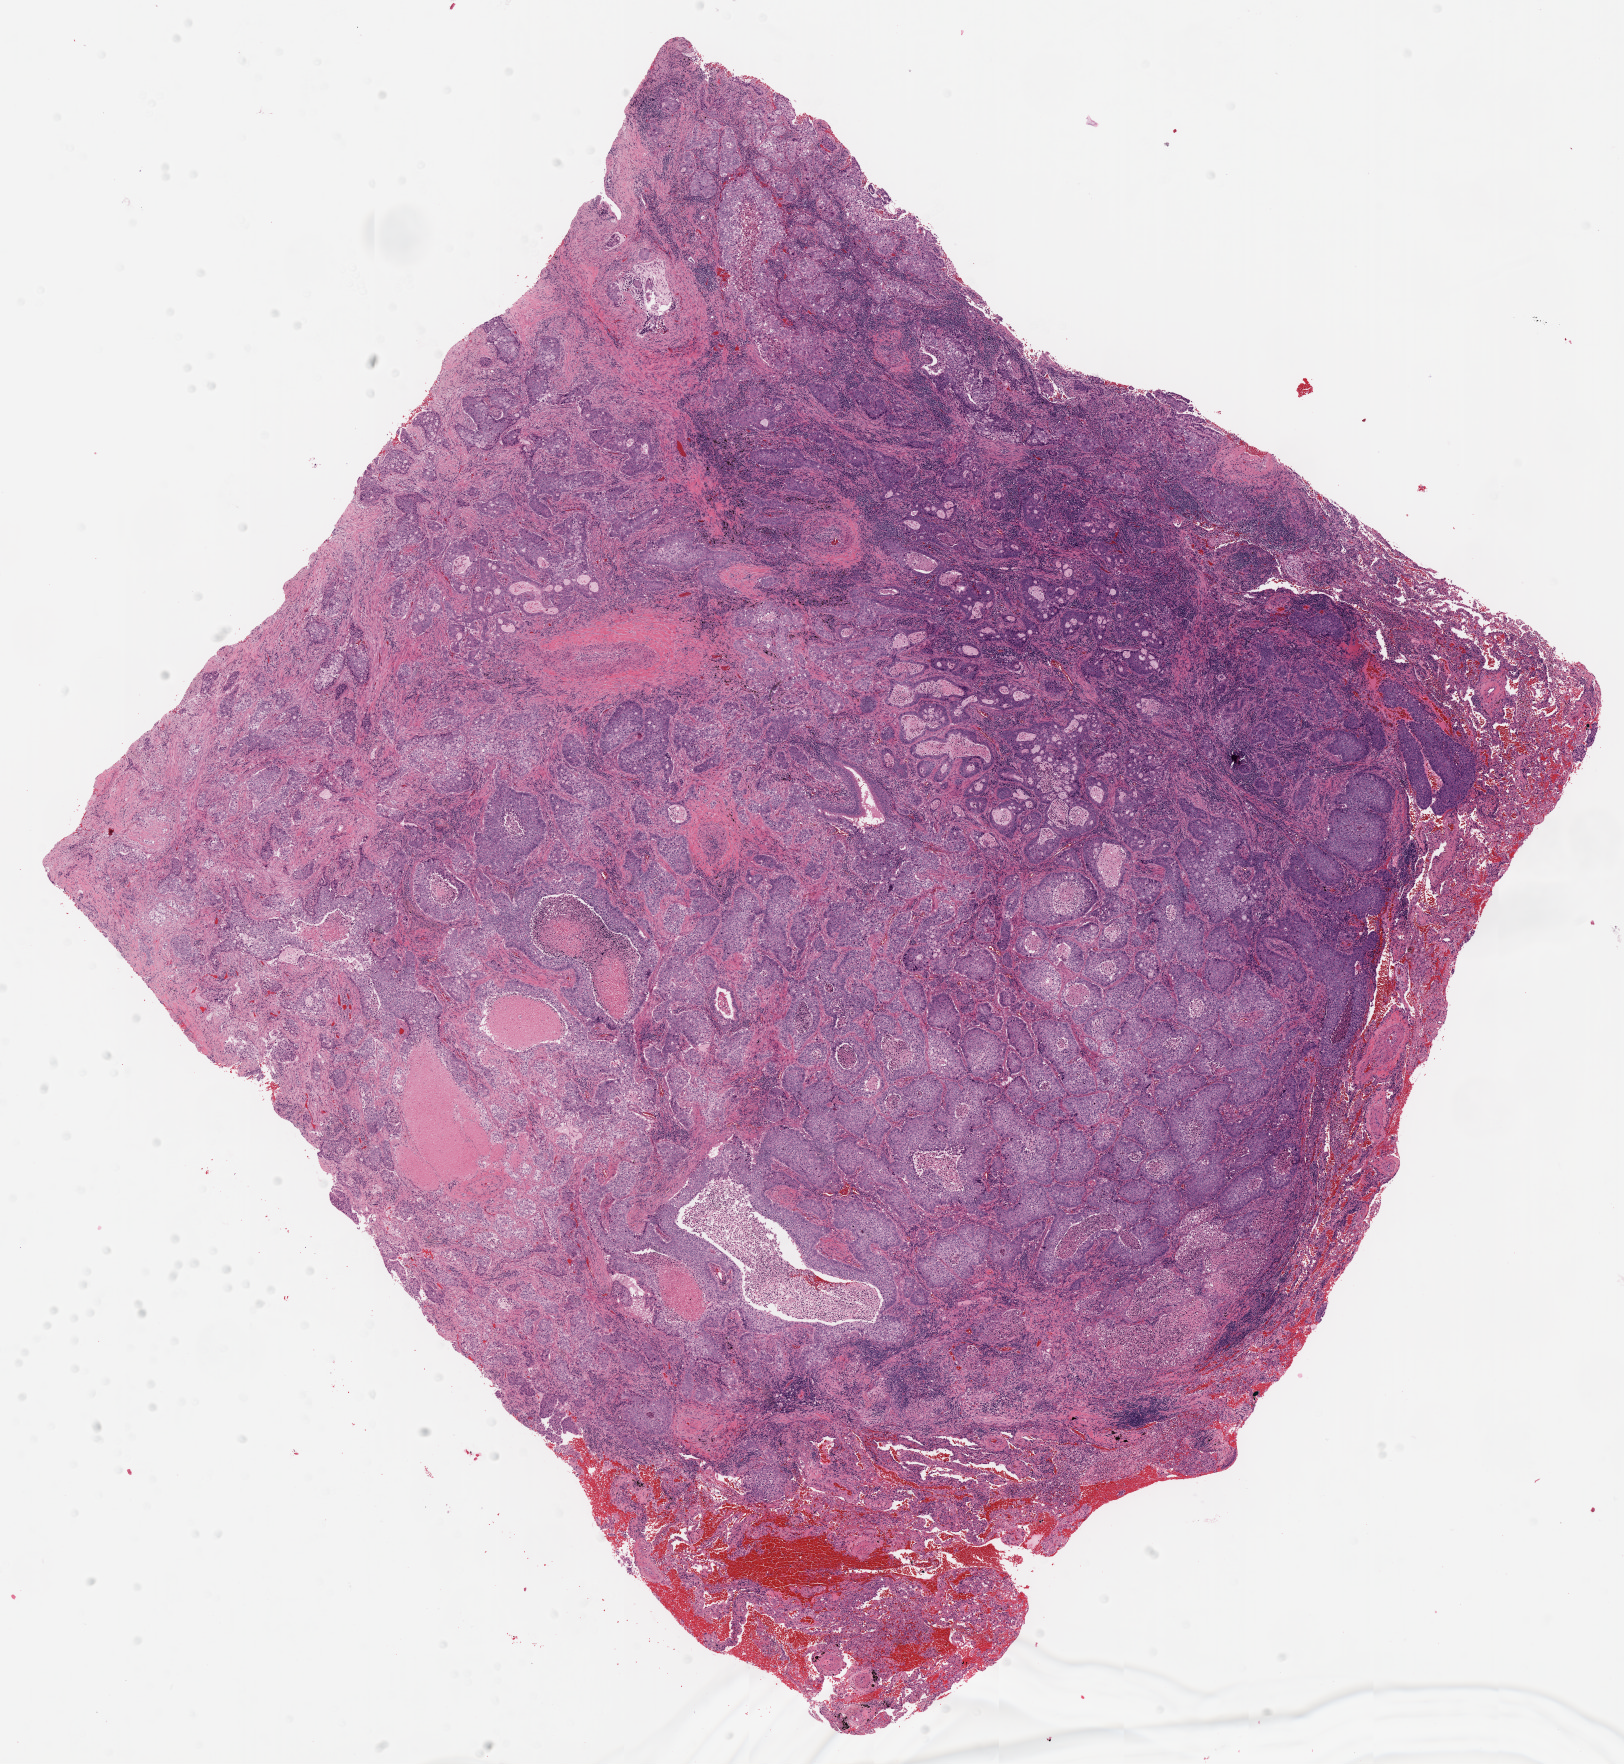
H&E-stained whole-slide image — whole scanned area (about 13.0 x 14.1 mm, acquisition: 20x scan) shown as a low-resolution overview, formalin-fixed paraffin-embedded (FFPE) diagnostic section, sample: primary tumour, lung. Patient sex: male.
Pathologic diagnosis: Adenocarcinoma, NOS (lower lobe, lung). AJCC pathologic stage: IB (6th edition).